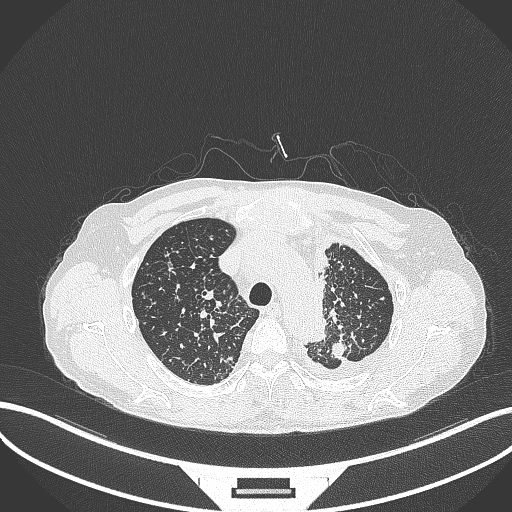
Chest CT, one axial slice; position 274 of 325 along the scan axis; reconstruction kernel B70f; 120 kVp; lung window (W 1500 / L -600 HU); 1 mm slice thickness; 512 × 512 image matrix, field of view 400 × 400 mm. Male patient, age 58 years. From the clinical record (not read from this slice): clinical TNM (as recorded): T1c N3 M1.
Structures marked on this image (rectangle marked by the reading radiologist):
- lung tumour (recorded histology: adenocarcinoma): bounding box [x1, y1, x2, y2] px = [326, 332, 352, 361]